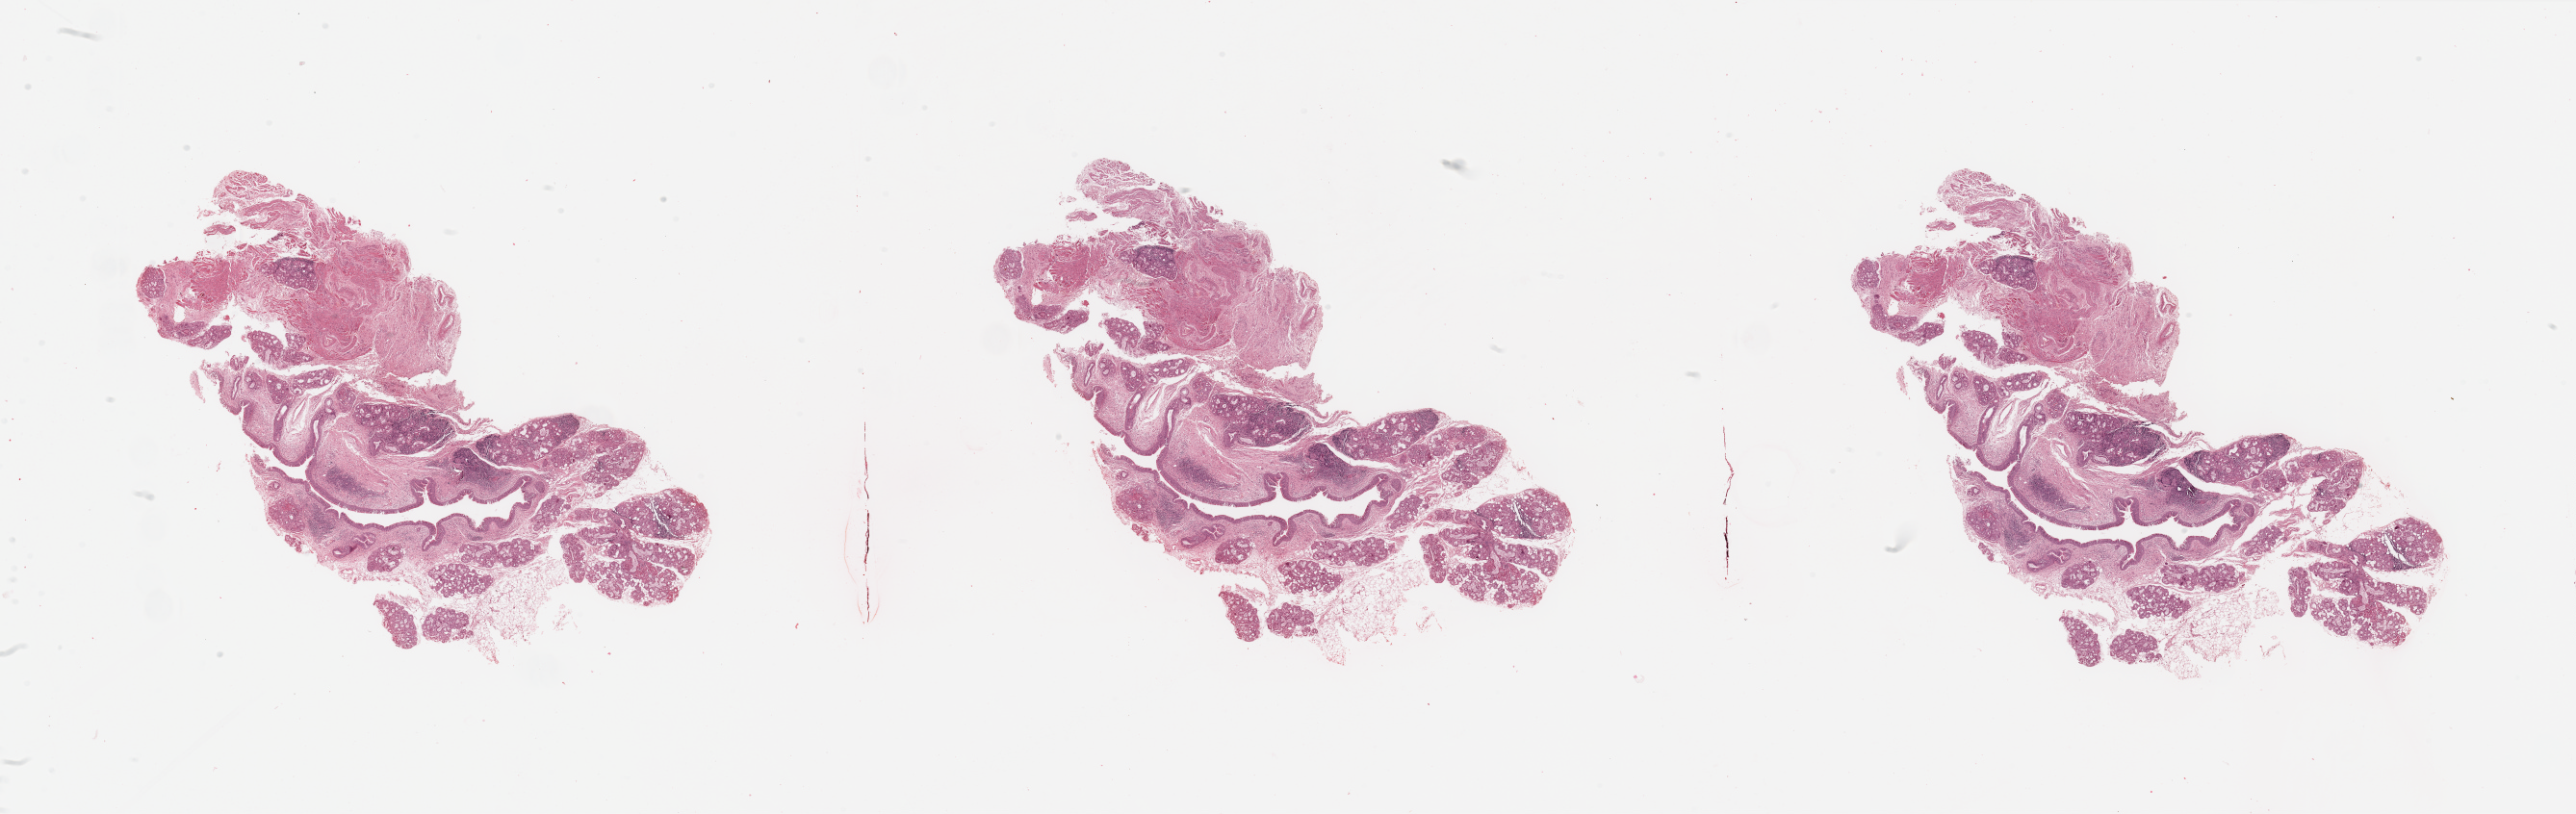
Whole-slide histology image, Hematoxylin and eosin (H&E) stained, whole scanned area (about 42.3 x 13.4 mm, acquisition: 20x scan) shown as a low-resolution overview. Normal (non-tumour) tissue sample, sampled site: larynx. Male, 60 y/o.
• this section: normal (non-tumour) tissue from the same patient
• patient diagnosis: Squamous cell carcinoma, NOS (larynx, NOS)